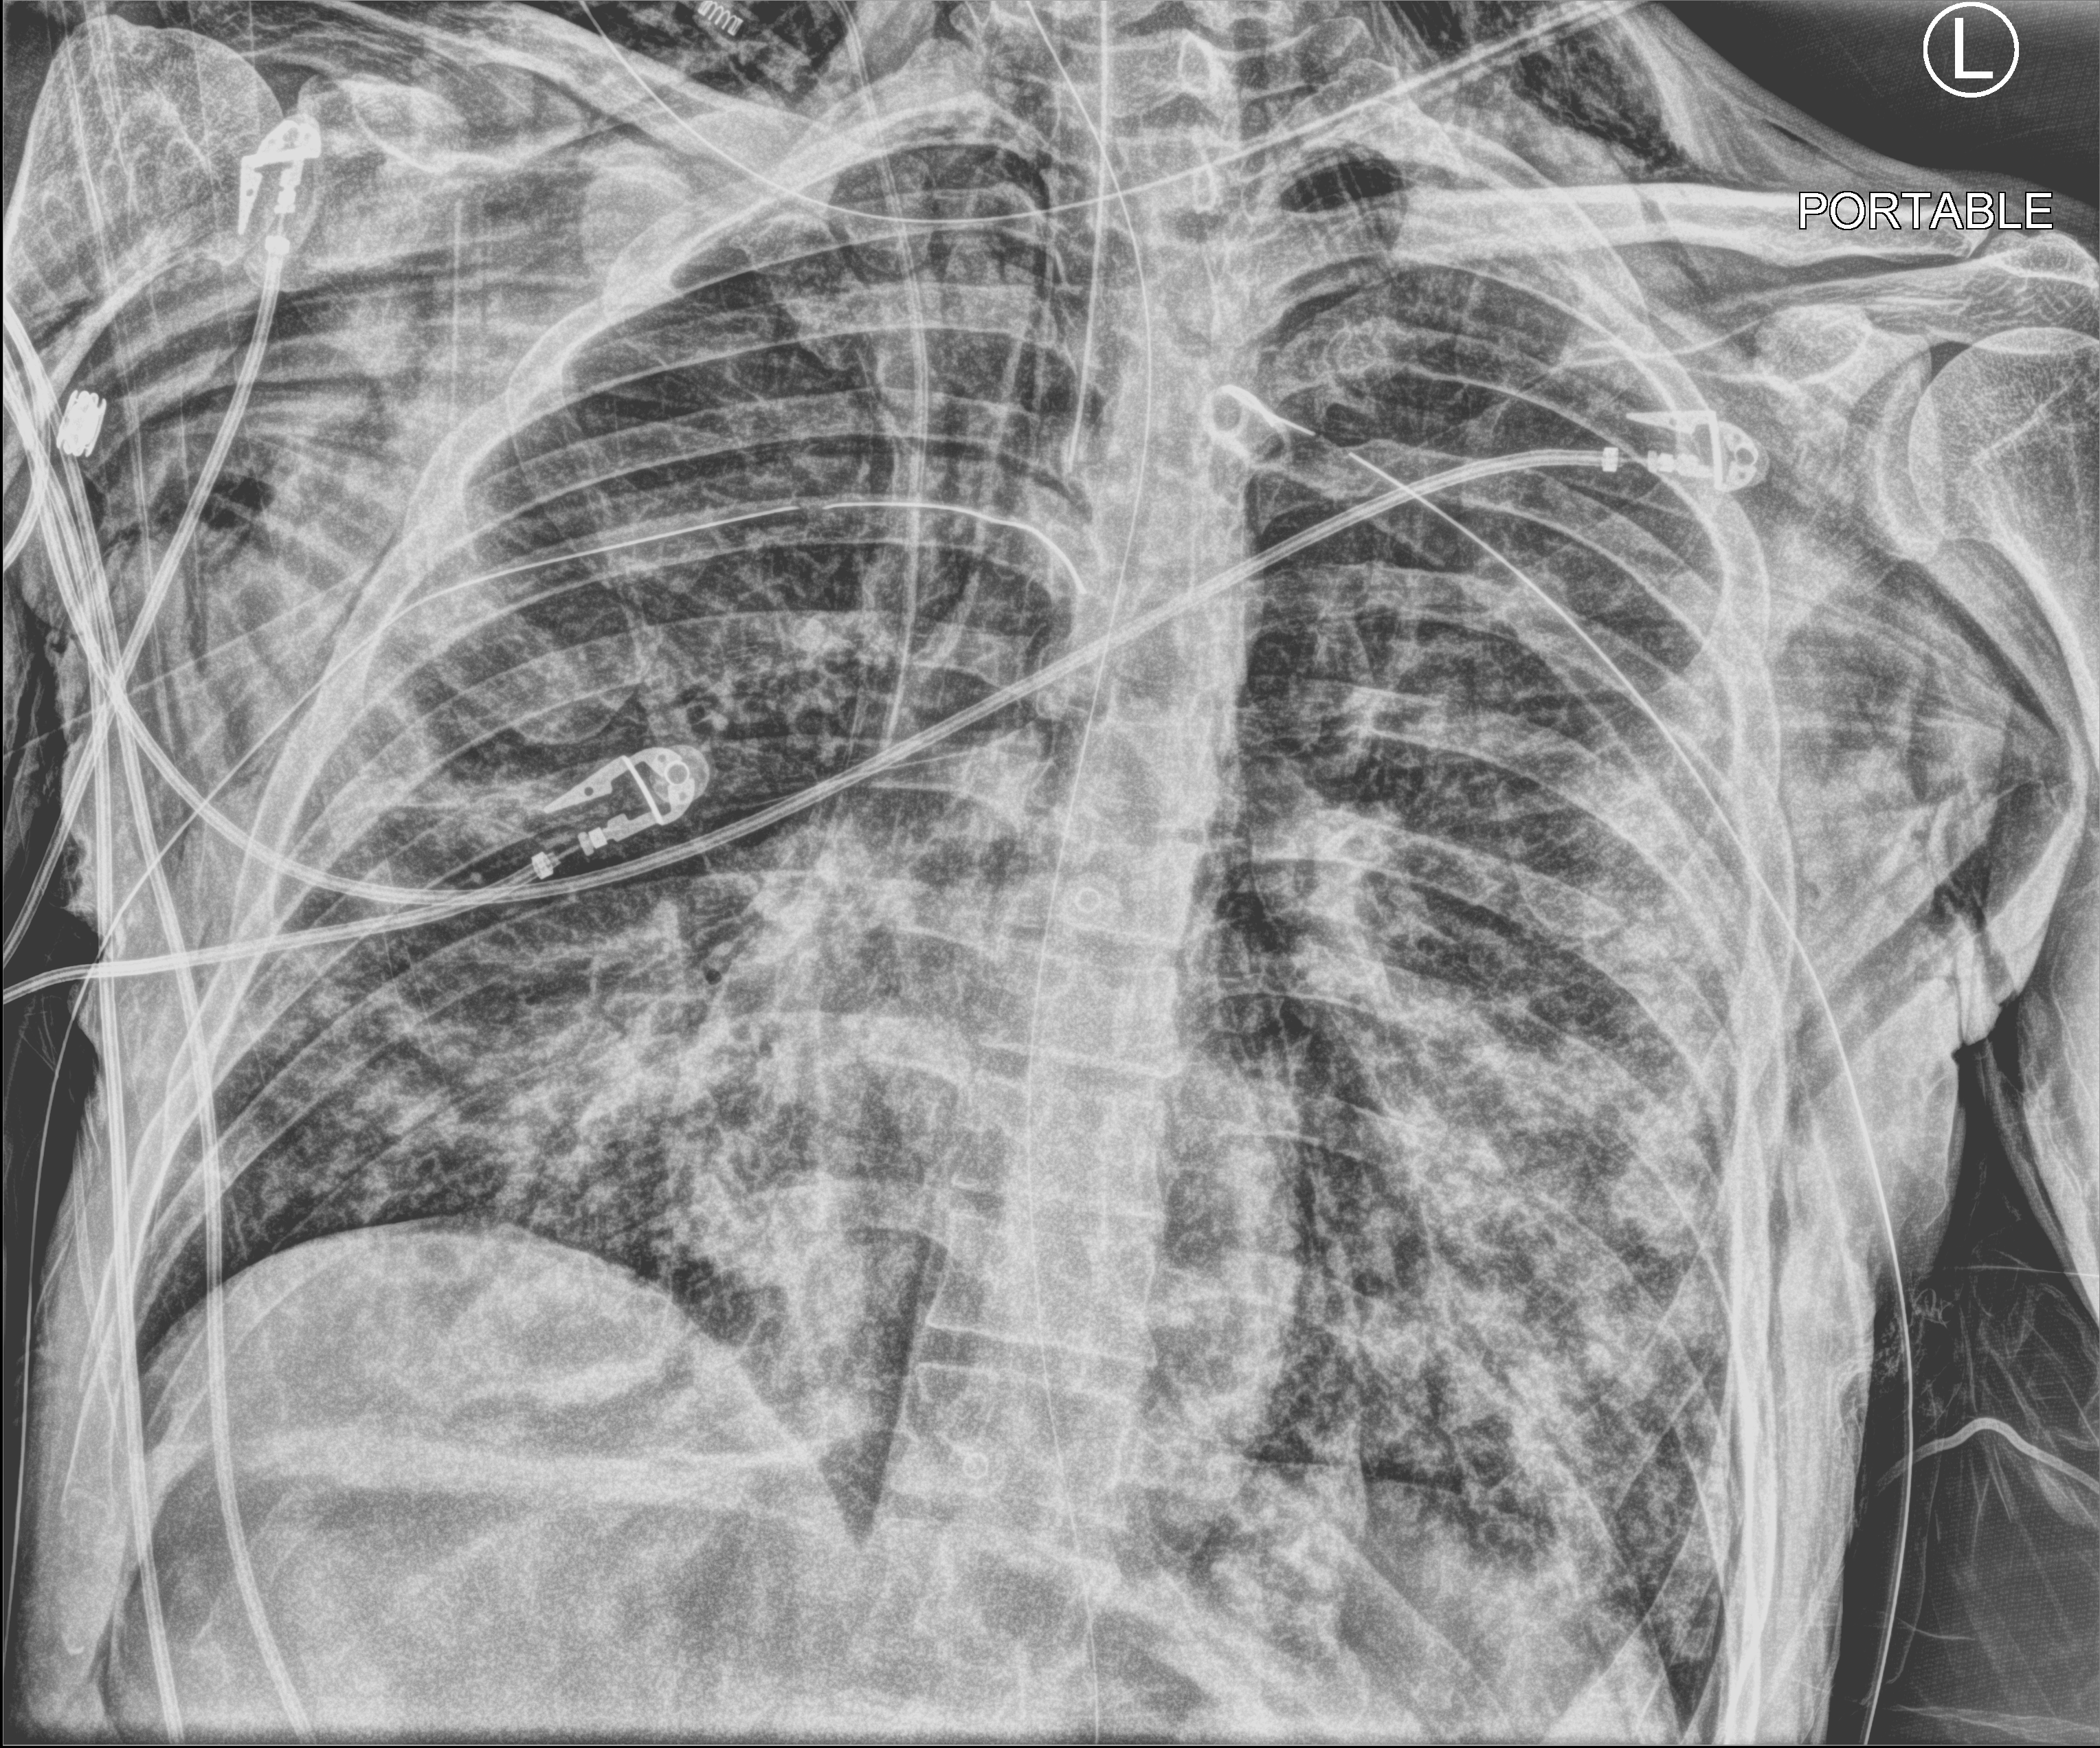
Chest X-ray (portable), anteroposterior (AP) projection. Patient hospitalised with COVID-19; male, aged 18–59 years.
Hospital-stay facts (about this admission, not read from this image; timing relative to this image not recorded): other chronic lung disease (admission record): no; length of hospital stay: 96 days.